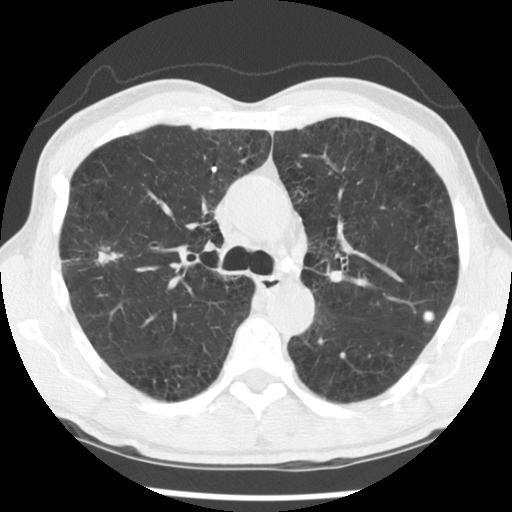
Low-dose screening chest CT, one axial slice; slice 86 of 138 in the series (ordered by position); lung window (W 1500 / L -600 HU); 2.5 mm slice thickness; 512 × 512 image matrix, field of view 320 × 320 mm.
Structures marked on this image (outlined manually by an expert reader):
- lesion 1 (tumor, upper lobe of right lung): bounding box (x1, y1, x2, y2) in pixels: (96, 247, 123, 265)